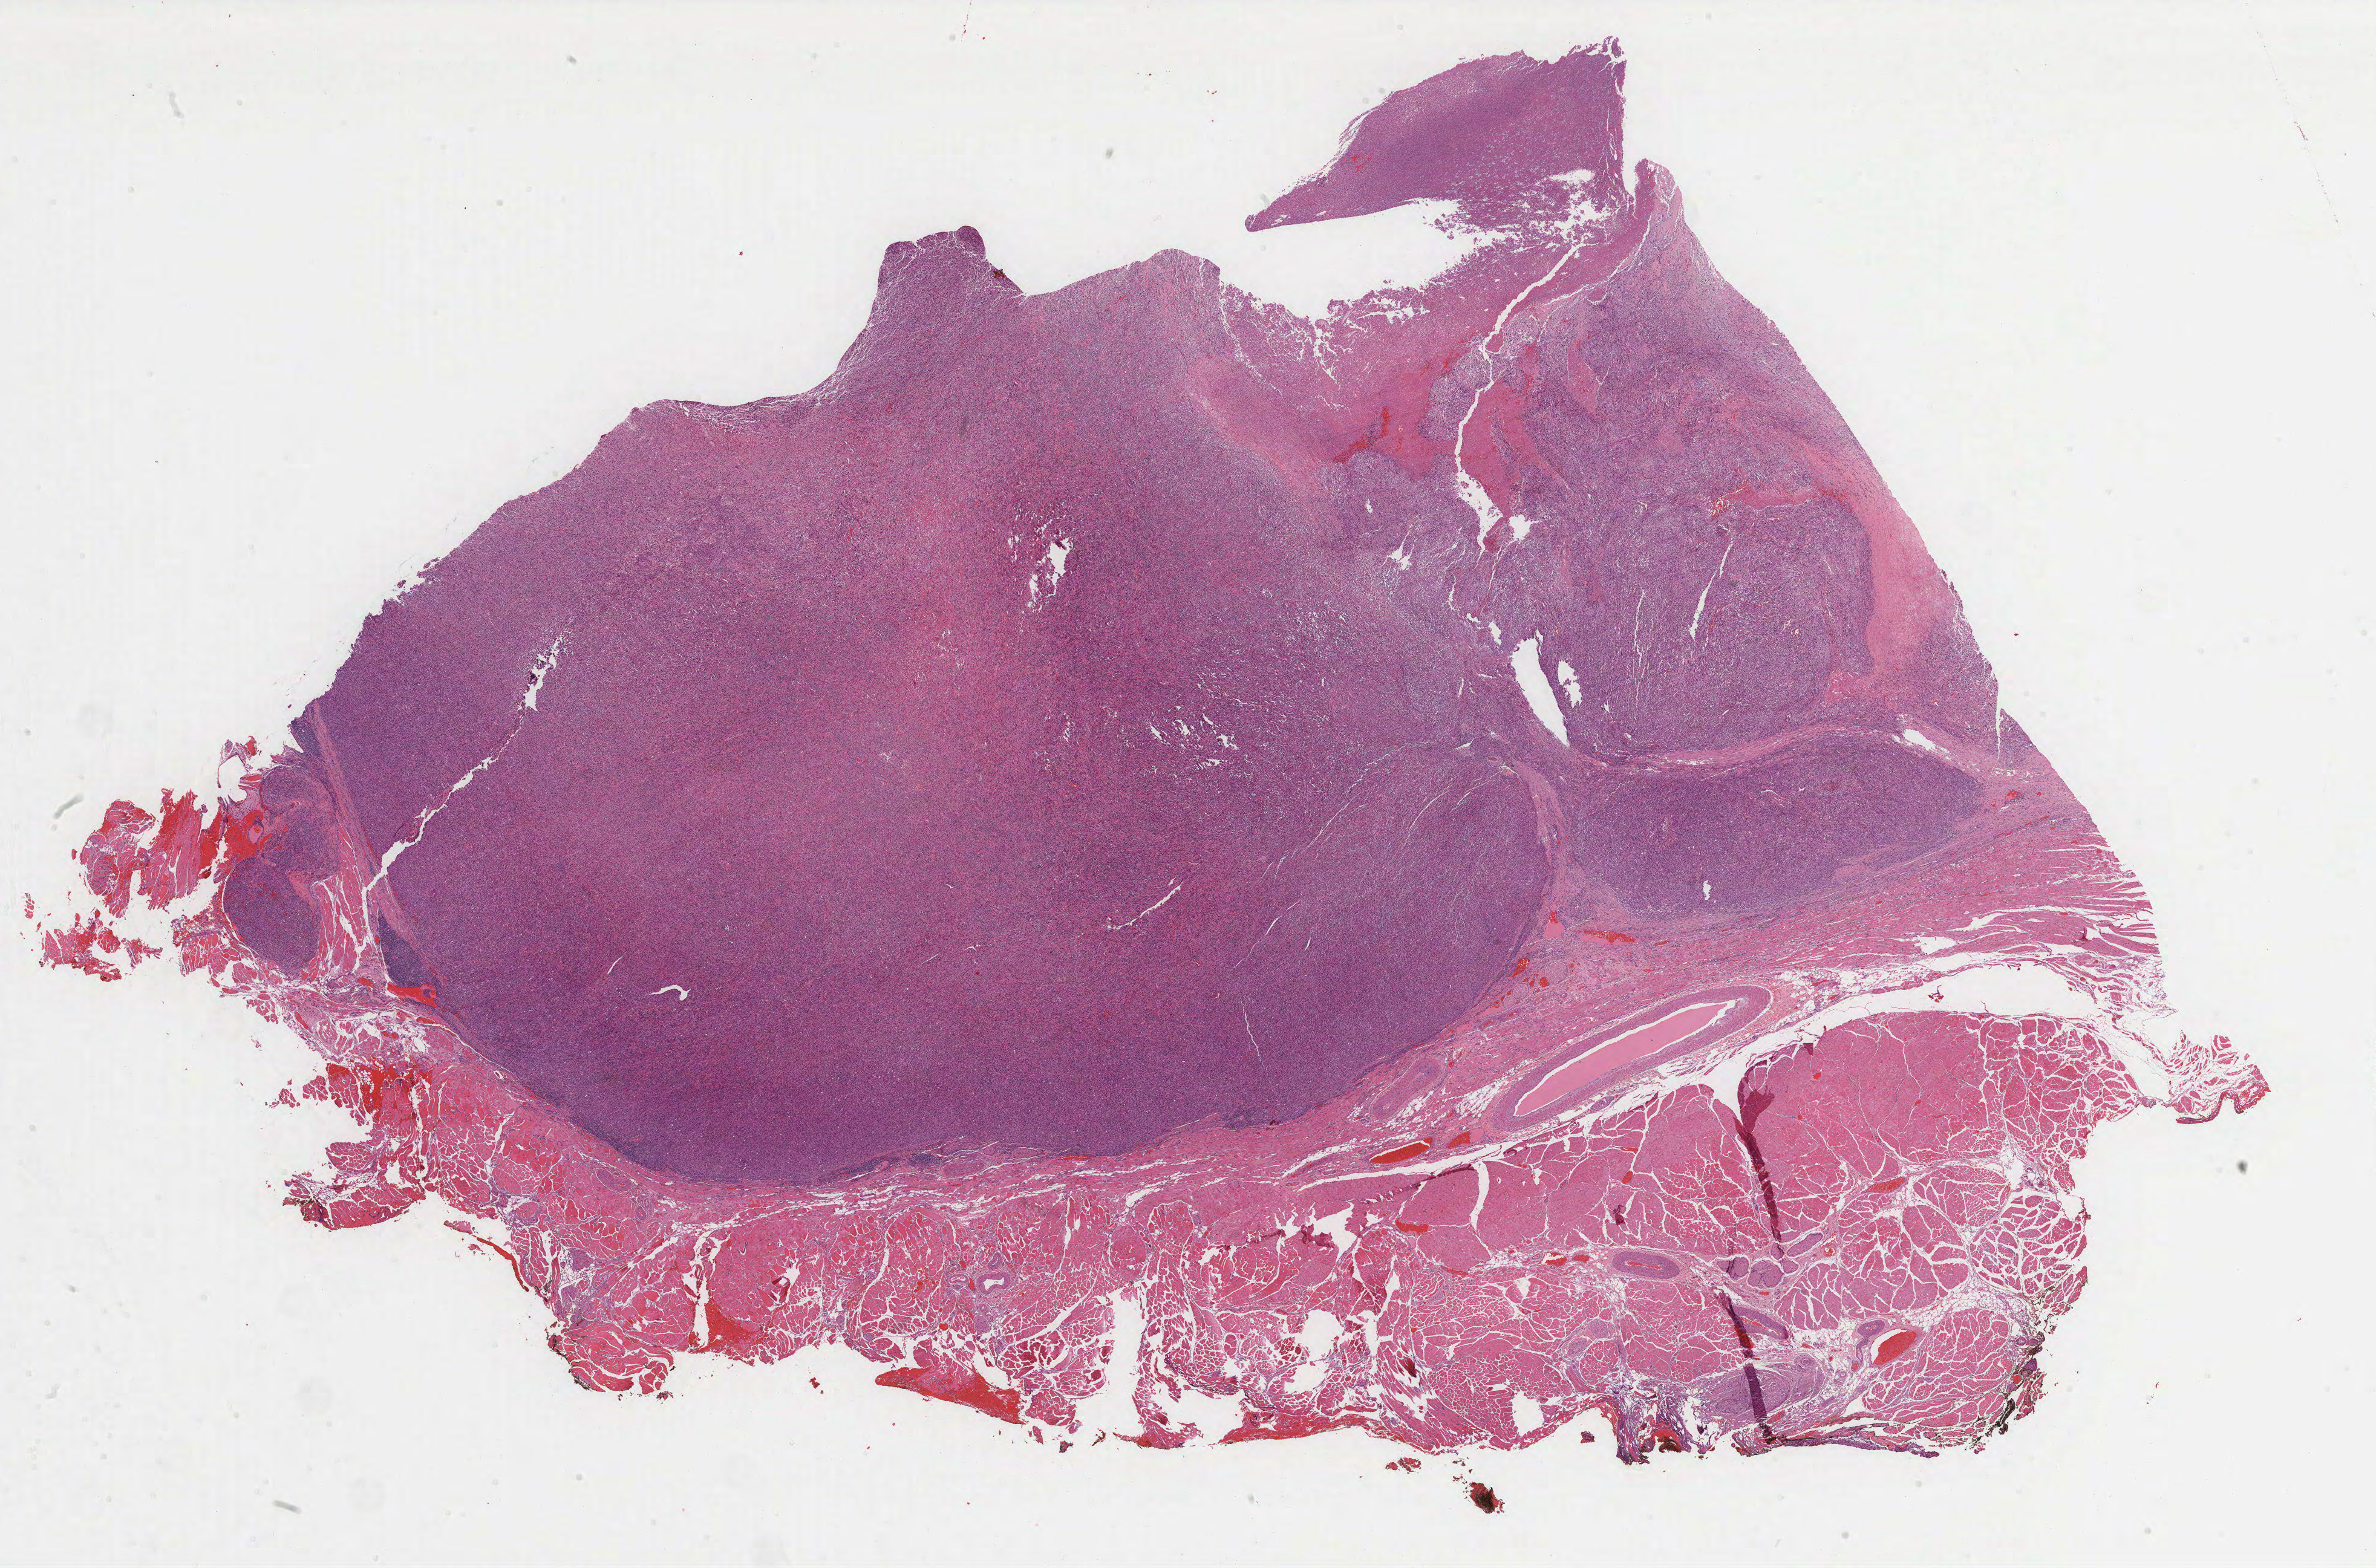
Hematoxylin and eosin (H&E) stained whole-slide image, whole scanned area (about 31.7 x 20.9 mm, slide scanned at 40x) shown as a low-resolution overview; formalin-fixed paraffin-embedded (FFPE) diagnostic section; other and unspecified parts of tongue, primary tumour sample. Patient: male, age at initial diagnosis 53 years.
Diagnosis: Leiomyosarcoma, NOS (tongue, NOS).